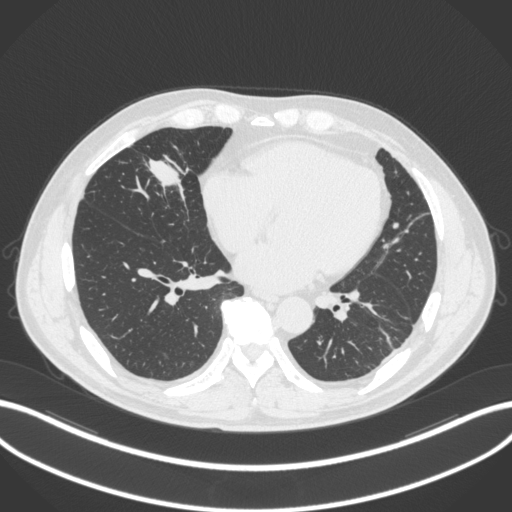
Chest CT, one axial slice. Position 105 of 399 along the scan axis. 120 kVp. Lung window (W 1500 / L -600 HU). 1 mm slice thickness. 512 × 512 image matrix, field of view 400 × 400 mm. Male patient, age 59 years. Case-level facts recorded for this patient, not image findings: clinical TNM (as recorded): T2a N1 M0.
Annotated regions visible in this slice (rectangle marked by the reading radiologist):
- lung tumour (recorded histology: adenocarcinoma): bounding box (x1, y1, x2, y2) in pixels: (140, 152, 191, 201)